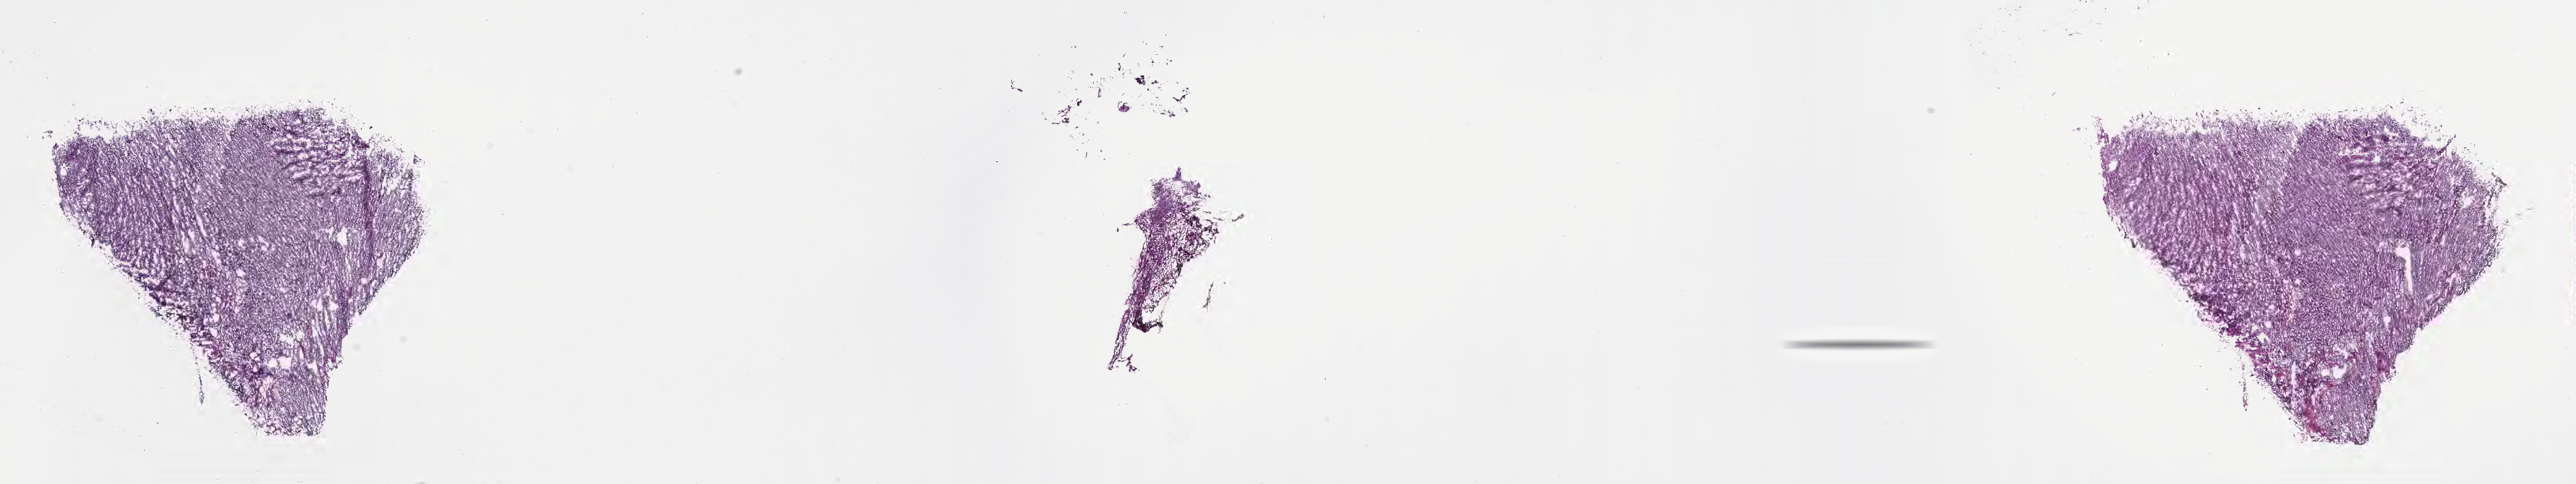
Hematoxylin and eosin (H&E) whole-slide image of tumor tissue from the brain — low-resolution overview of the scanned area, about 30.7 x 5.8 mm. Frozen section. Patient: male, age 53 months (4 years 5 months).
Diagnosis: Medulloblastoma, NOS.